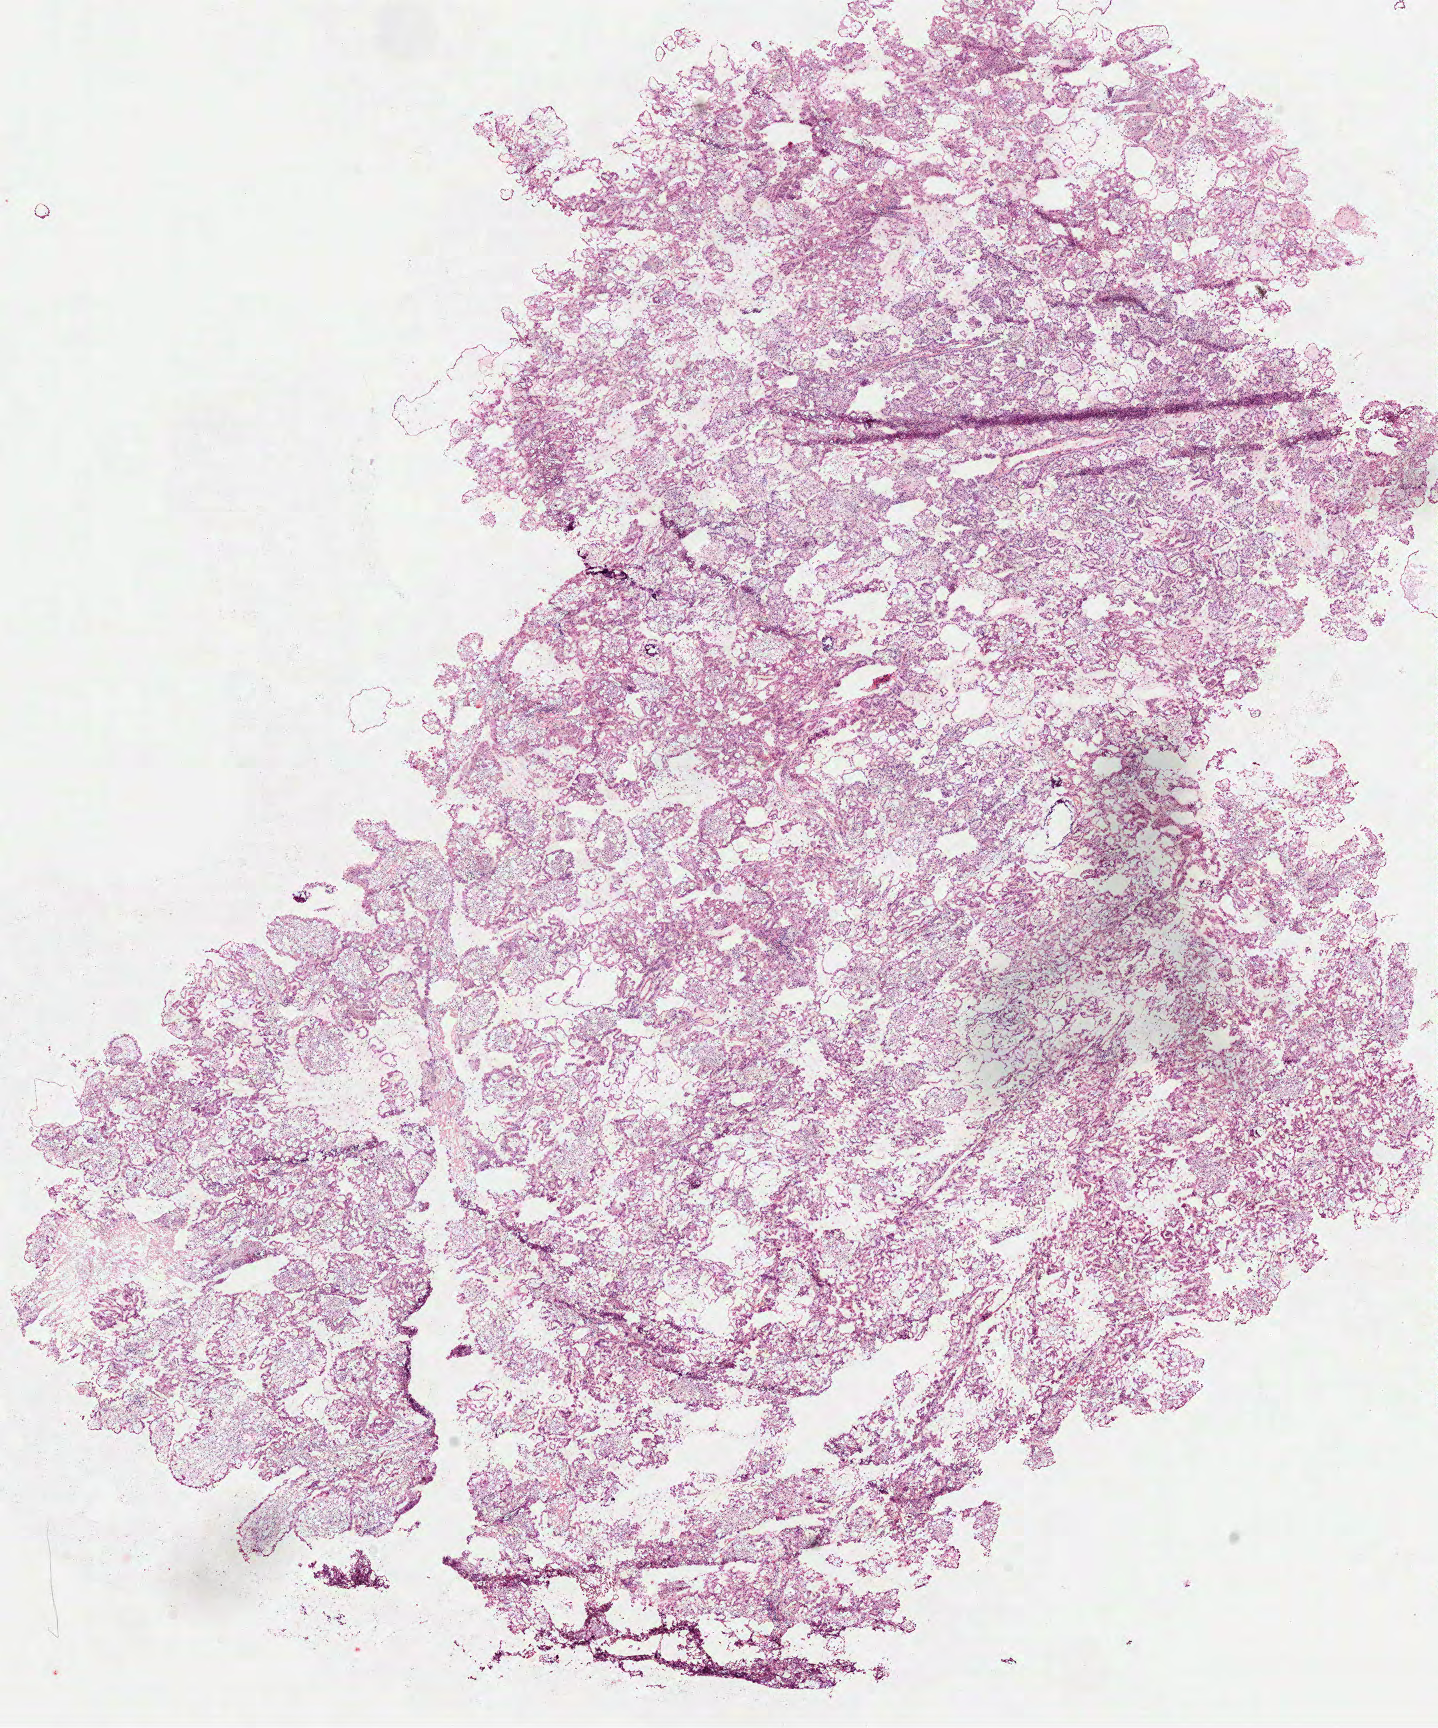
Digitized H&E-stained tissue section (whole slide), a low-resolution overview of the entire scanned area, about 11.6 x 13.9 mm (slide scanned at 40x), frozen section from the top of the tissue portion, primary tumour sample from the kidney. Male patient; age at initial diagnosis 61 years.
Histologic diagnosis: Papillary adenocarcinoma, NOS.